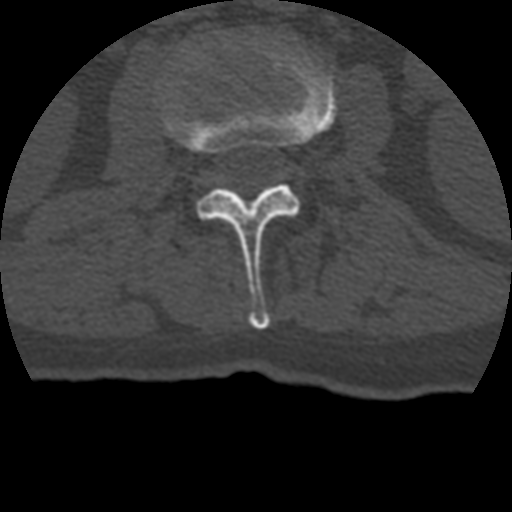
CT including the spine, one axial slice; slice 110 of 399 in the series (ordered by position); 120 kVp; bone window (W 1800 / L 400 HU); 1.25 mm slice thickness; 512 × 512 image matrix, field of view 160 × 160 mm. Patient age 69 years. Case-level facts recorded for this patient, not image findings: primary cancer: prostate.
Annotated regions visible in this slice (semi-automatic segmentation, software-assisted and operator-edited):
- L2 vertebra: bounding box <162,40,335,329> (left, top, right, bottom; pixels)